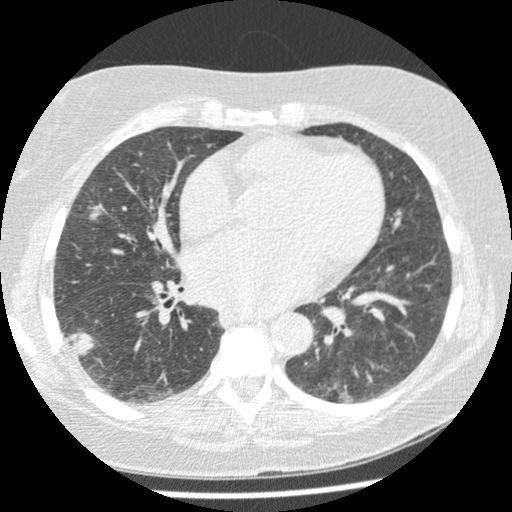
Low-dose screening chest CT, one axial slice. Position 113 of 241 along the scan axis. 120 kVp. Lung window (W 1500 / L -600 HU). 512 × 512 image matrix.
Structures marked on this image (expert manual segmentation):
- lesion 1 (tumor, lower lobe of right lung): bounding box [x1, y1, x2, y2] px = [71, 331, 96, 356]